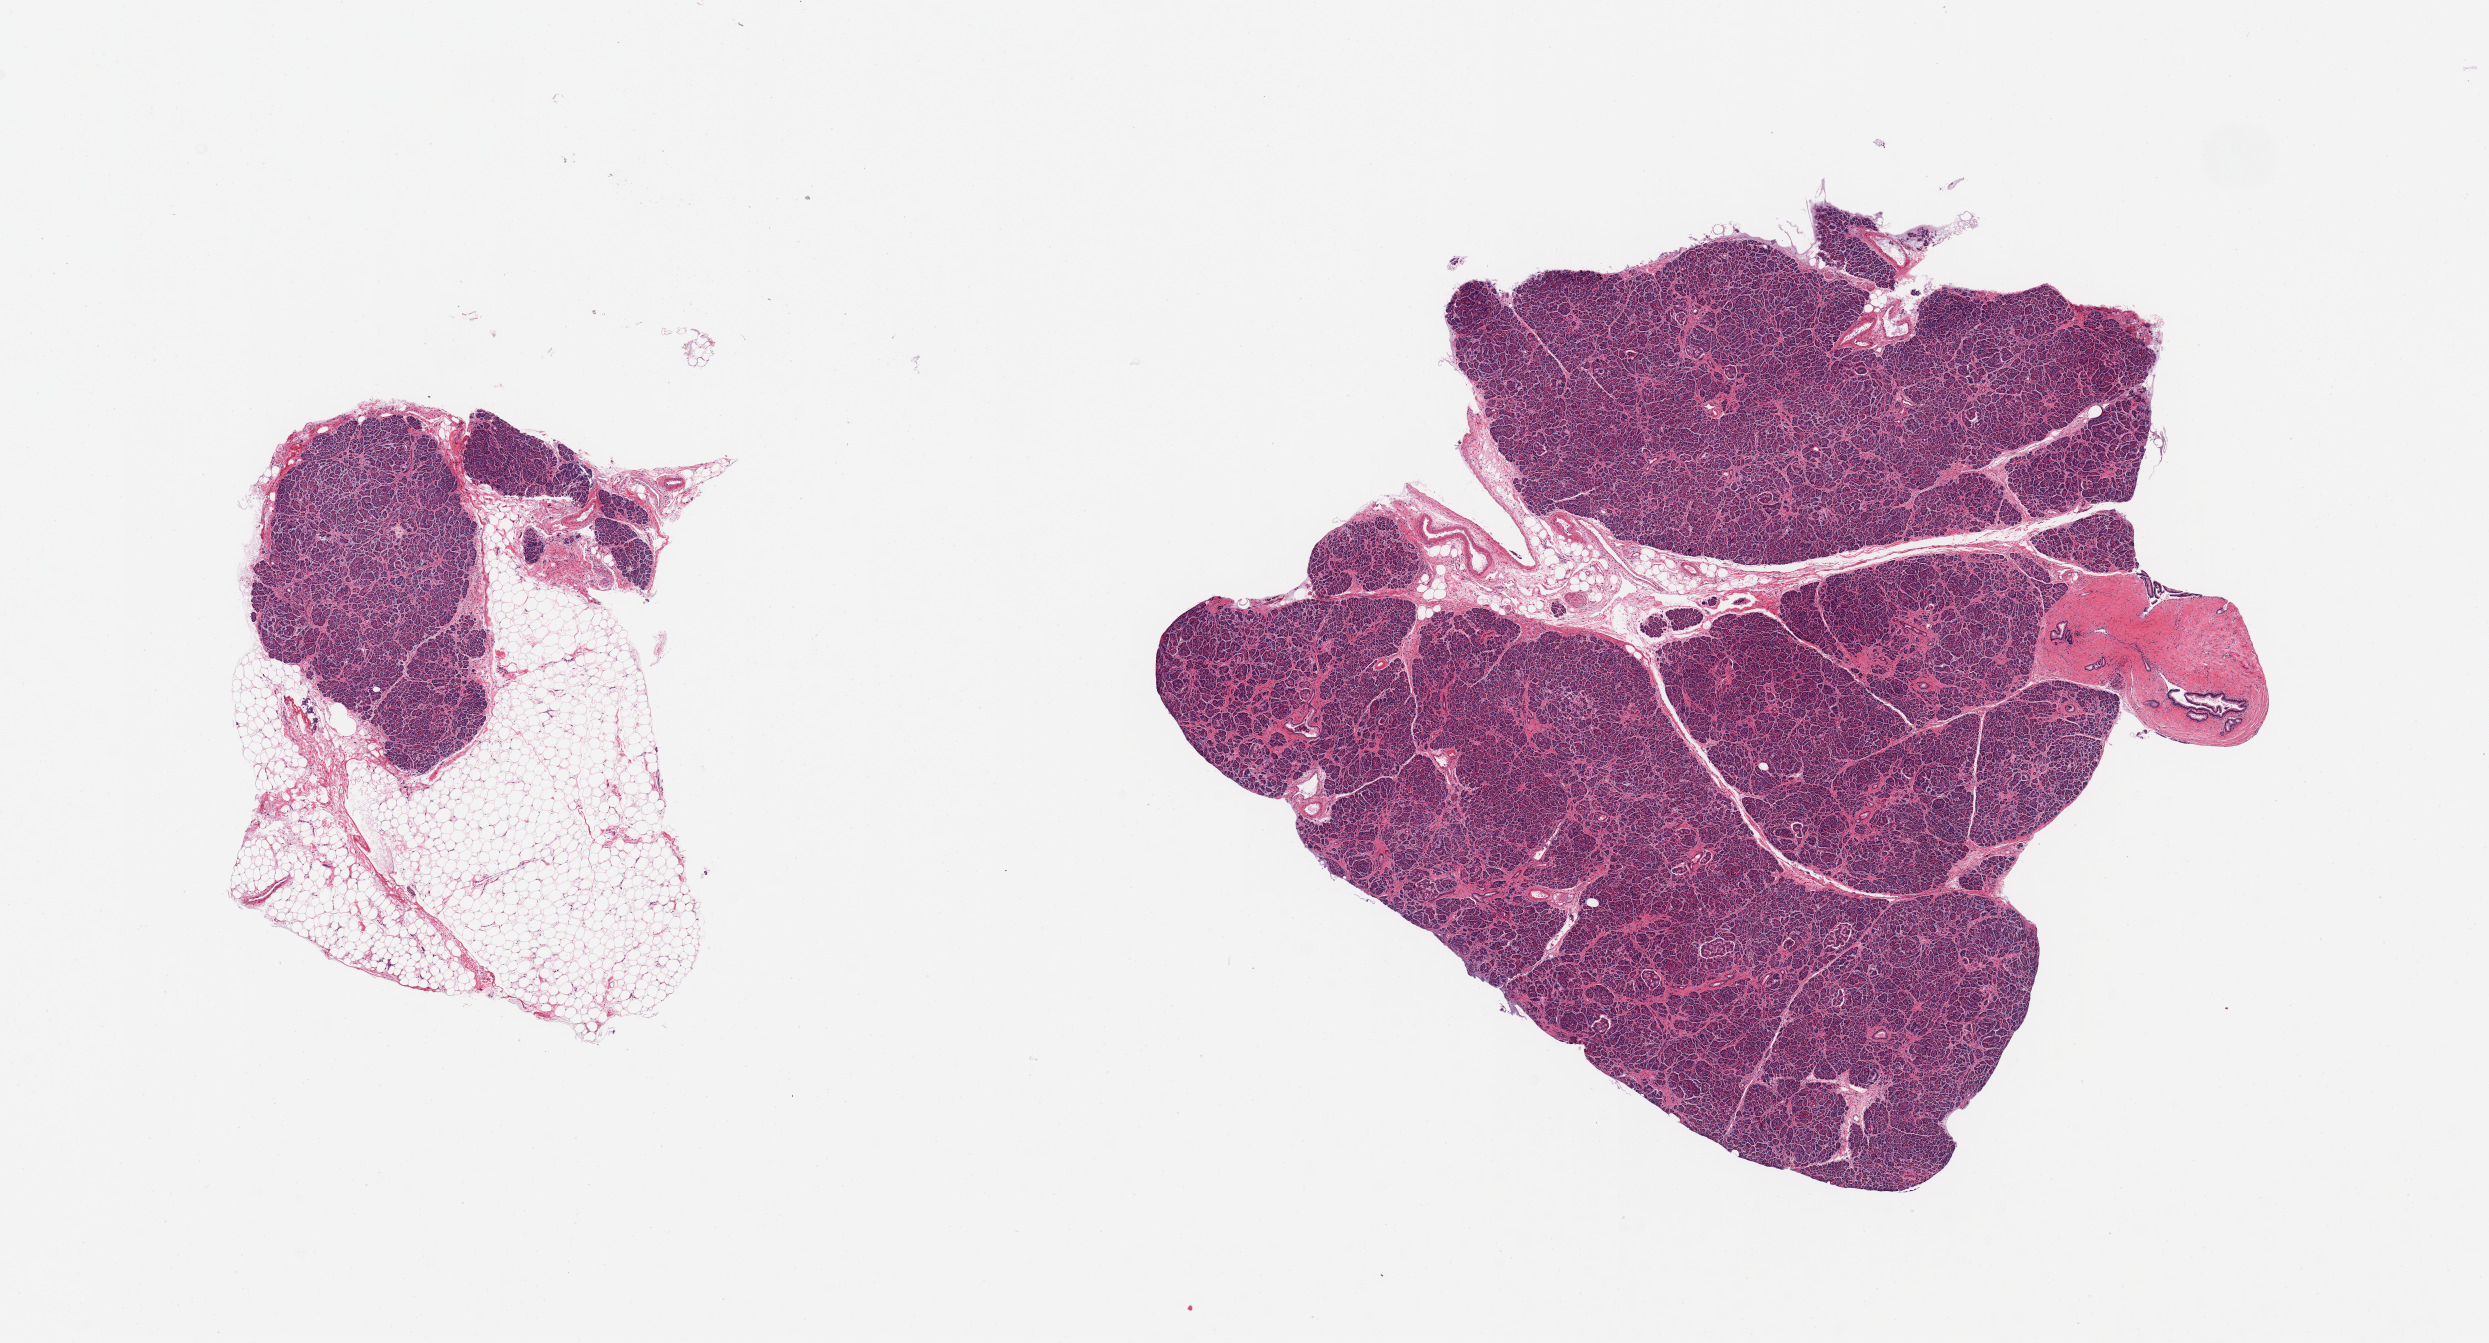
Haematoxylin and eosin whole-slide image, brightfield — low-resolution overview of the scanned area, about 19.7 x 10.6 mm (acquisition: 20x scan). PAXgene-fixed paraffin-embedded (PFPE) section. Sampled site (target tissue): pancreas. Tissue donor sample. Male donor.
Reviewer comment on this tissue sample: 2 pieces; smaller piece is 50% fat/50% parenchyma, islets are well visualized, mild intralobular fibrosis.